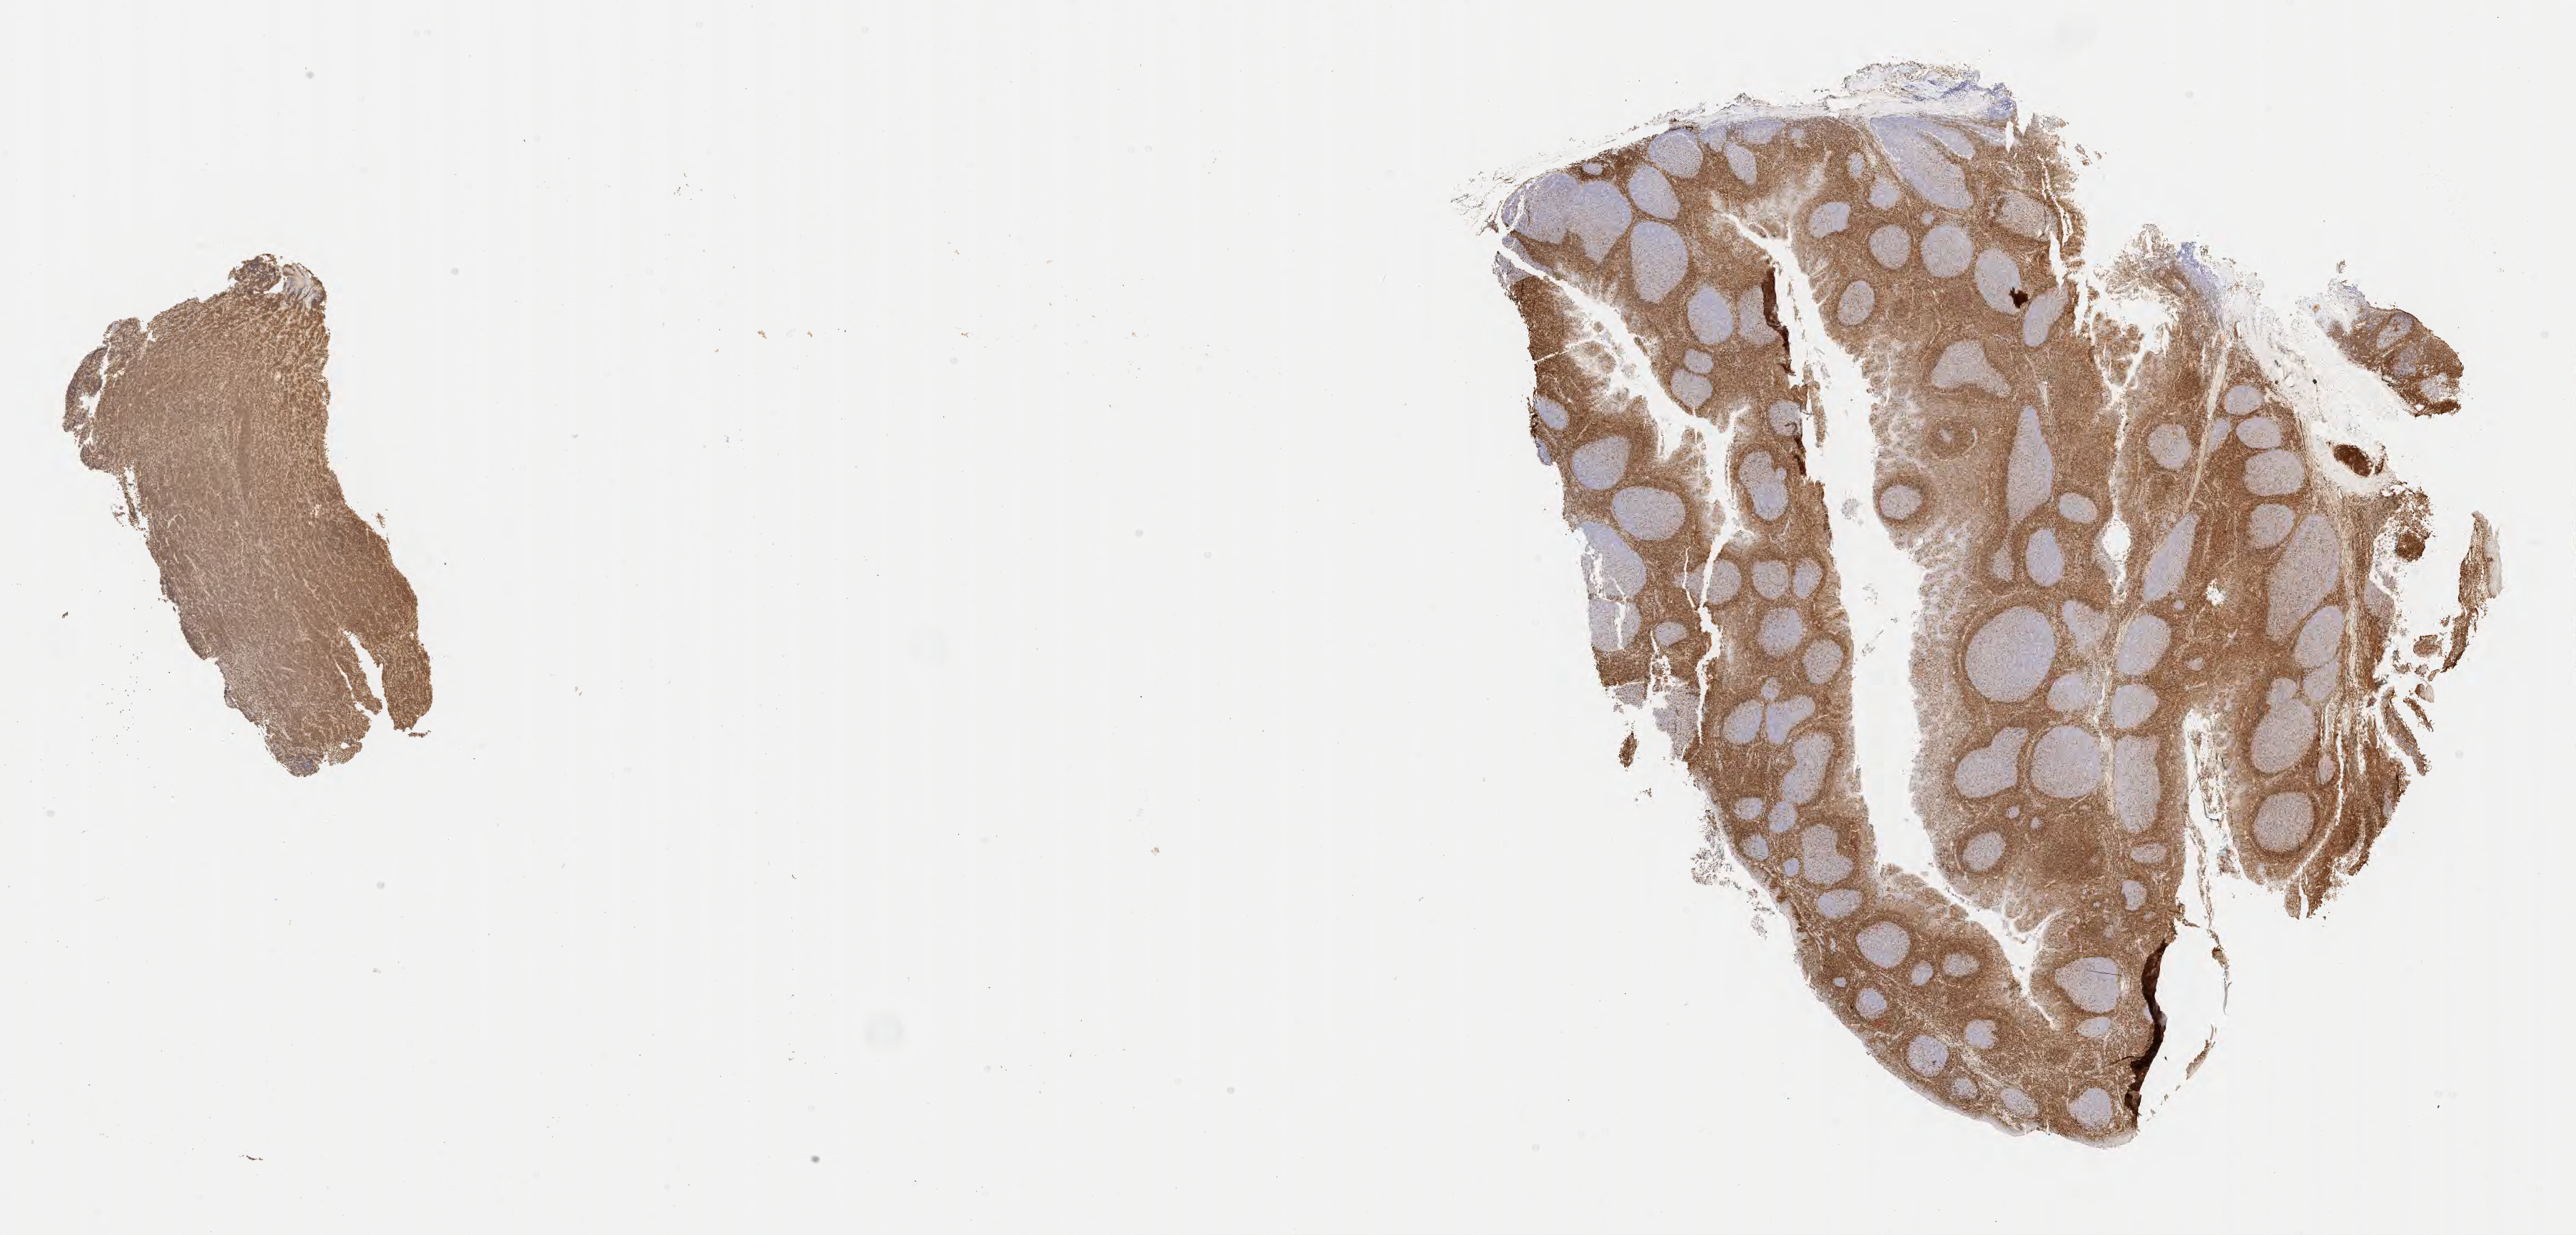
Immunohistochemistry (IHC) whole-slide image stained for BCL2, low-resolution overview of the scanned area, about 29.2 x 14.0 mm. Tumor tissue. Anatomic site: cranium. Patient male; age 11 years.
• diagnosis: Diffuse large B-cell lymphoma, NOS